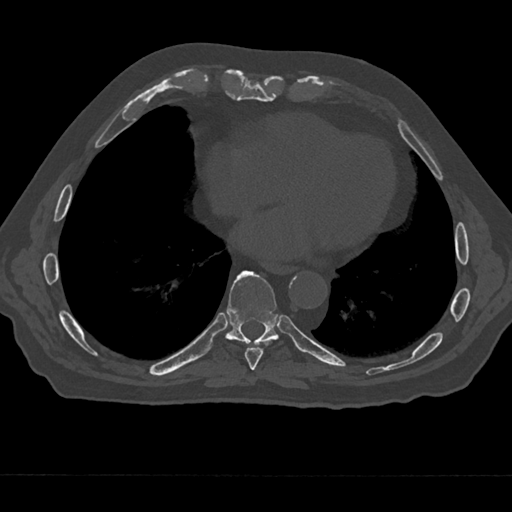
CT including the spine, one axial slice. Position 286 of 797 along the scan axis. 120 kVp. Bone window (W 1800 / L 400 HU). 0.5 mm slice thickness. 512 × 512 image matrix, field of view 377 × 377 mm. Patient: male, 75 years. Case-level facts recorded for this patient, not image findings: primary cancer: renal; vertebrae with lytic lesions (as recorded): T4.
Outlined on this slice (semi-automatic segmentation, software-assisted and operator-edited):
- T8 vertebra: box from (x=244, y=341) to (x=270, y=370) px
- T9 vertebra: (x=221, y=270)–(x=283, y=349)